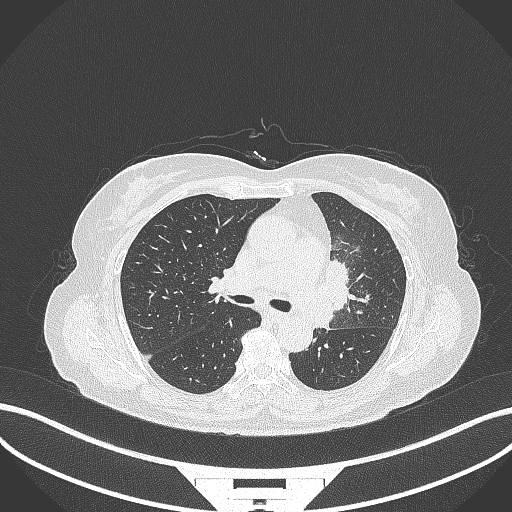
Chest CT, one axial slice. Position 205 of 382 along the scan axis. Reconstruction kernel B70f. 120 kVp. Lung window (W 1500 / L -600 HU). 512 × 512 image matrix, field of view 400 × 400 mm. Female patient, age 64 years. From the clinical record (not read from this slice): clinical TNM (as recorded): T2a N2 M0.
Annotated regions visible in this slice (rectangle marked by the reading radiologist):
- lung tumour (recorded histology: adenocarcinoma): bounding box <316,253,349,332> (left, top, right, bottom; pixels)